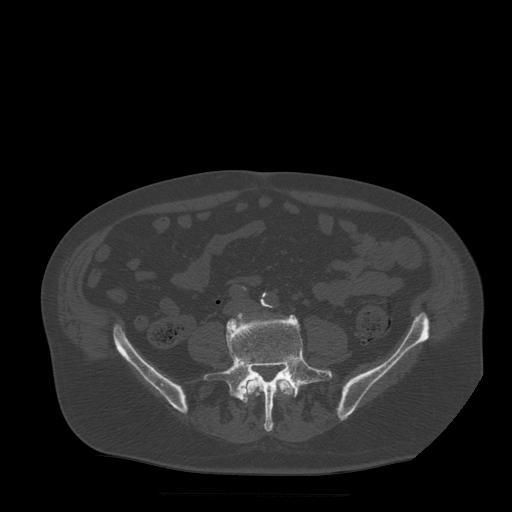
CT including the spine, one axial slice; slice 95 of 522 in the series (ordered by position); bone window (W 1800 / L 400 HU); 1.25 mm slice thickness; 512 × 512 image matrix, field of view 420 × 420 mm. Patient age 72 years. From the clinical record (not read from this slice): primary cancer: prostate.
Annotated regions visible in this slice (semi-automatic segmentation, software-assisted and operator-edited):
- L4 vertebra: box from (x=241, y=378) to (x=296, y=403) px
- L5 vertebra: (x=204, y=313)–(x=333, y=432)